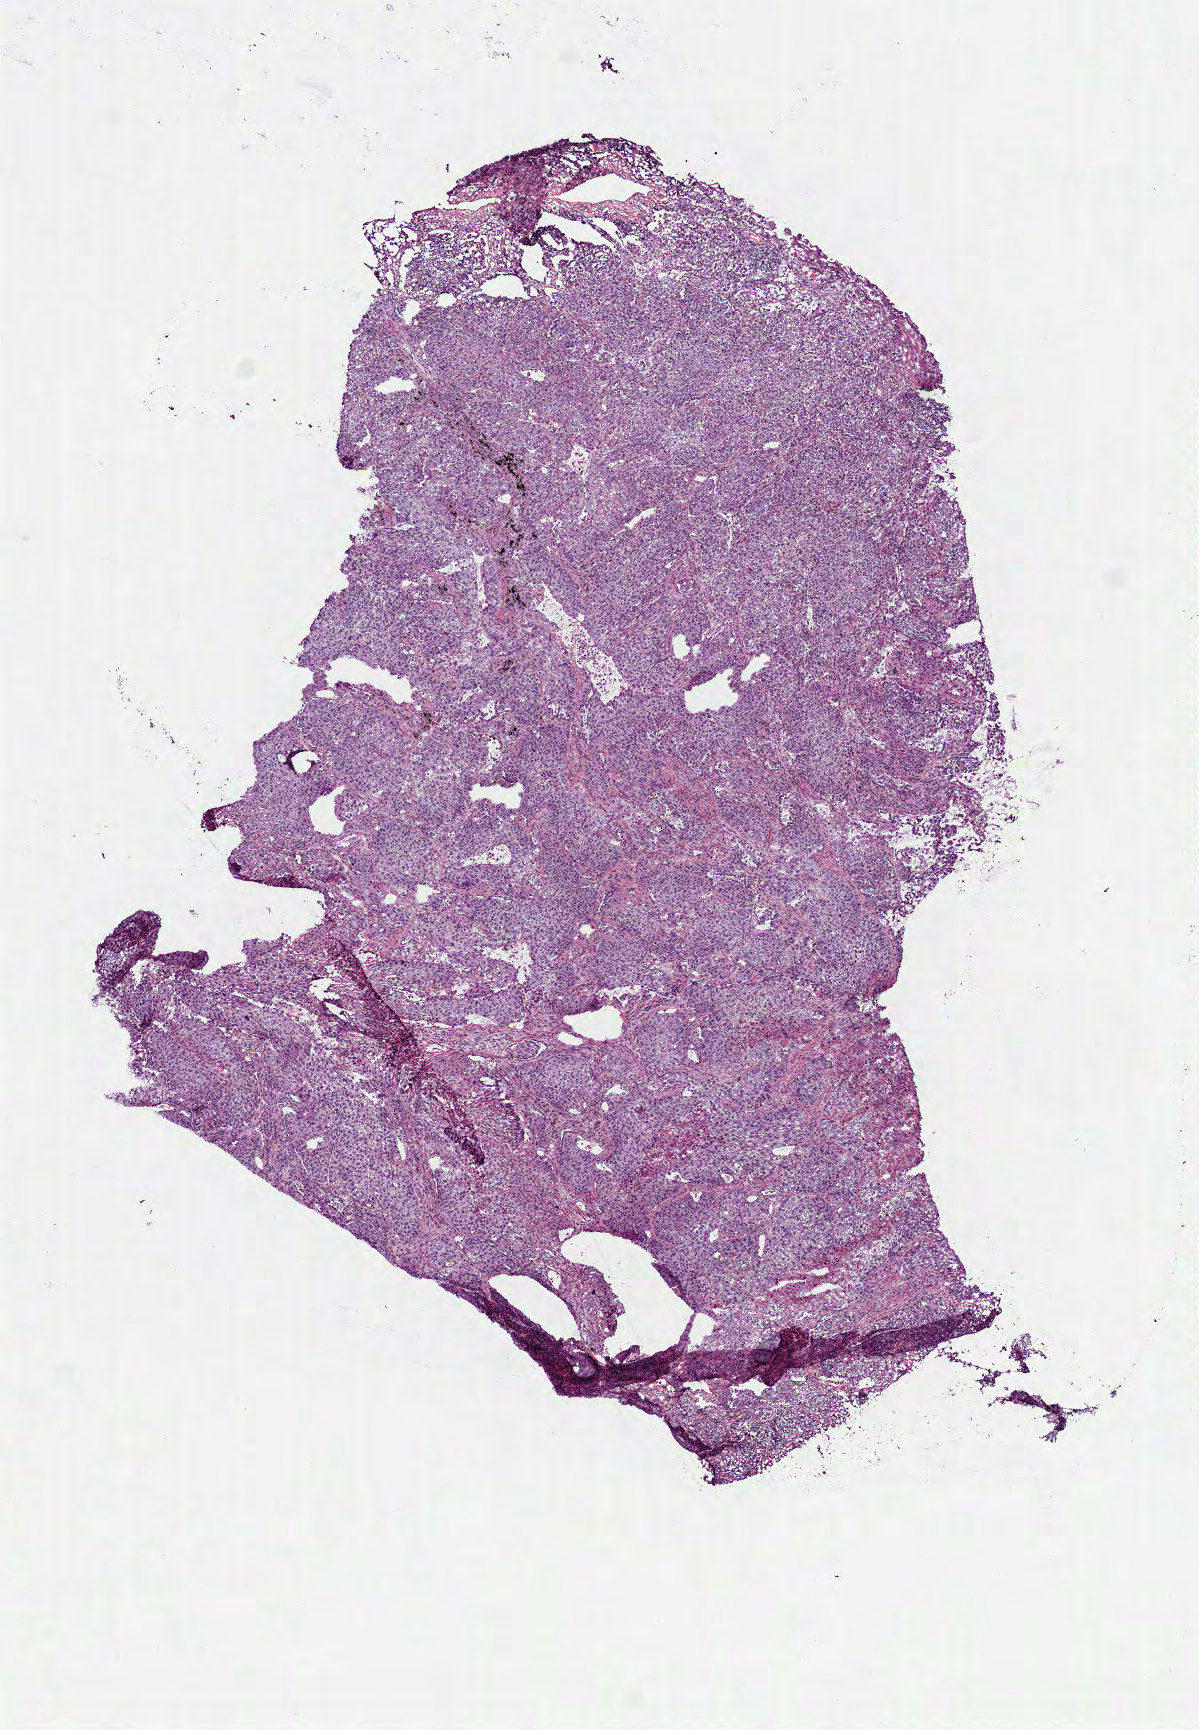
Digitized H&E tissue section (whole slide), a low-resolution overview of the entire scanned area, about 4.8 x 7.0 mm (from a 40x scan); frozen section from the bottom of the tissue portion; primary tumour sample from the lung. Patient sex: male. Composition of this section per pathologist review: tumour cells 98%, tumour nuclei 85%, normal cells 0%, stromal cells 0%, necrosis 2%. Infiltration values recorded for this section: lymphocyte infiltration 5%, monocyte infiltration 1%, neutrophil infiltration 1%.
AJCC pathologic stage: IA (6th edition). Laterality: right. TNM: T1 N0 M0. Pathologic diagnosis: Squamous cell carcinoma, NOS (upper lobe, lung).